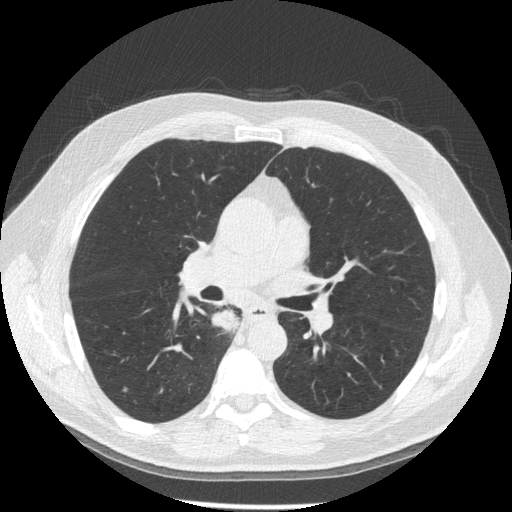
Low-dose screening chest CT, one axial slice; slice 104 of 181 in the series (ordered by position); lung window (W 1500 / L -600 HU); 512 × 512 image matrix, field of view 370 × 370 mm.
Outlined on this slice (manually delineated by an expert):
- lesion 1 (tumor, lower lobe of right lung): bounding box <212,310,240,332> (left, top, right, bottom; pixels)